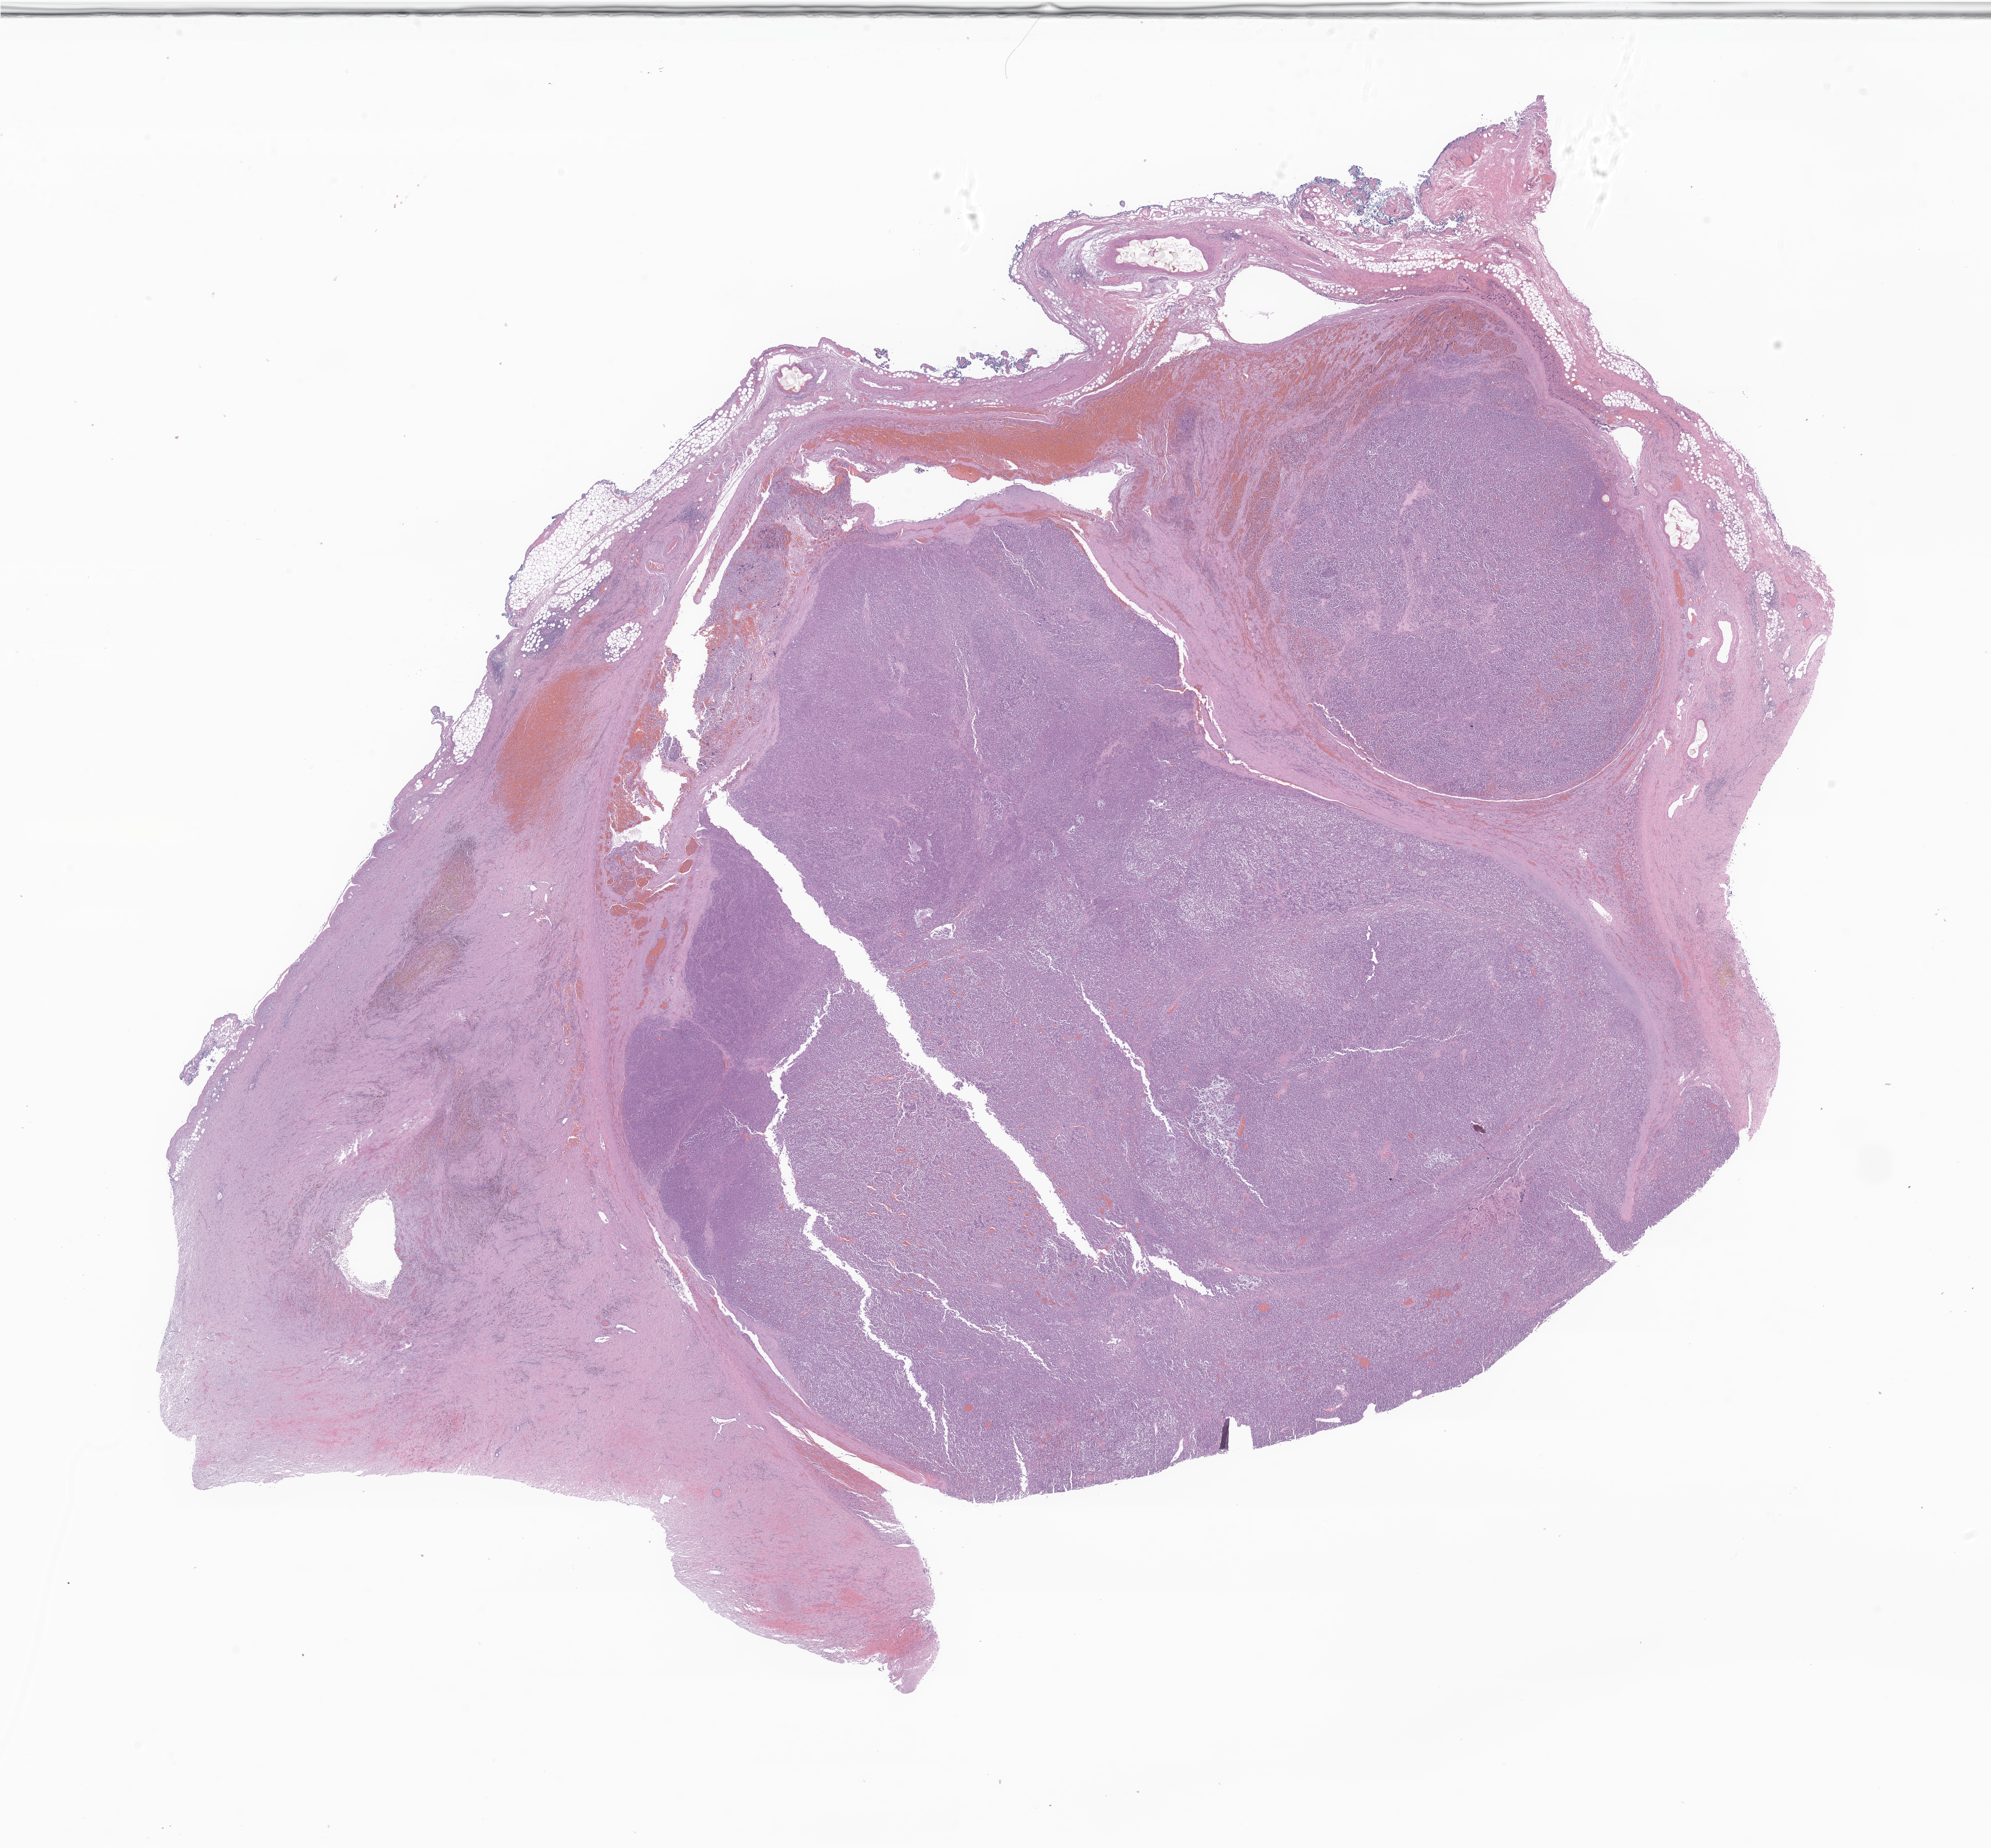
Whole-slide image, hematoxylin and eosin (H&E) stain of tumor tissue from the adrenal gland, whole scanned area (about 24.7 x 22.9 mm) shown as a low-resolution overview. Formalin-fixed paraffin-embedded section. Female patient, age 208 months (17 years 4 months).
Diagnosis (ICD-O-3 morphology term): Rhabdoid tumor, NOS.